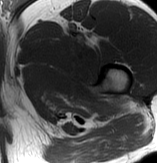
MRI of an extremity soft-tissue mass, one axial slice. MR volume resampled by the dataset authors to the PET/CT grid (not the native acquisition matrix). 3.27 mm slice thickness. 157 × 163 image matrix, field of view 153 × 159 mm. Male patient. From the clinical record (not read from this slice): histological type: extraskeletal osteosarcoma; grade: high; site of the primary tumour: left adductur.
Structures marked on this image (expert contour drawn on MRI and transferred to this co-registered scan by the dataset authors):
- gross tumour volume (mass): box from (x=49, y=24) to (x=128, y=120) px